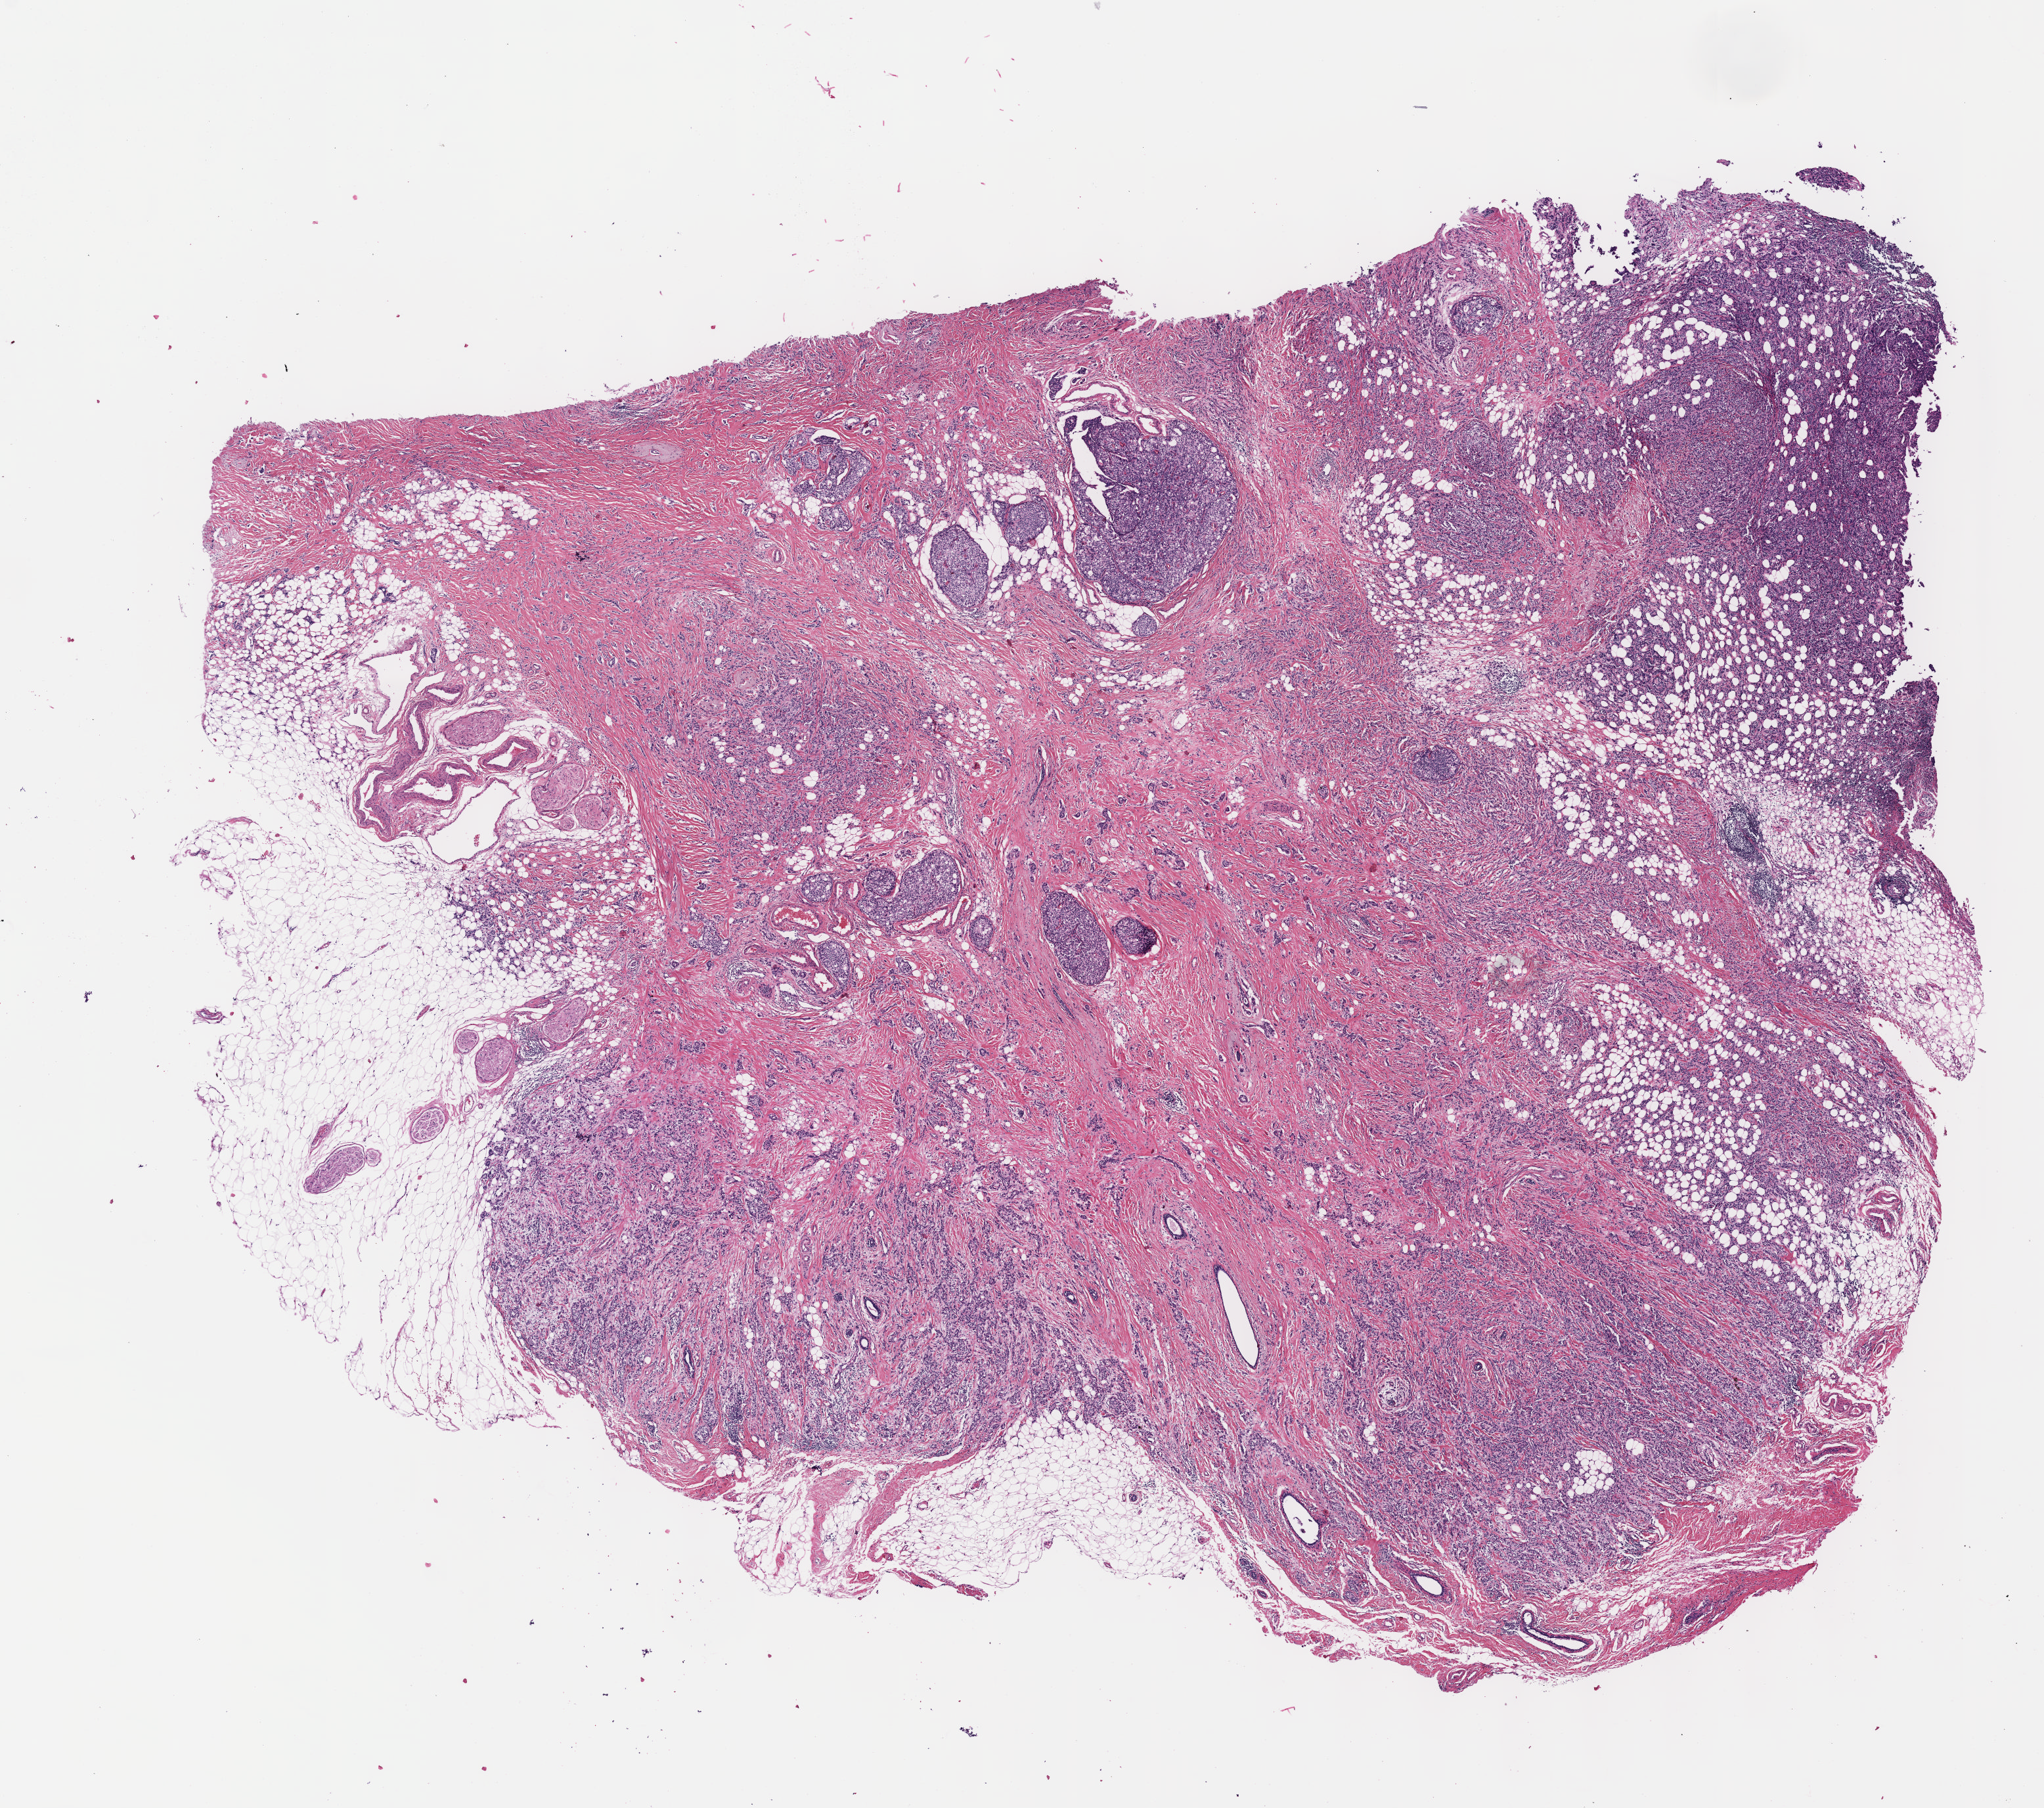
Whole-slide histology image, Hematoxylin and eosin (H&E) stained — whole scanned area (about 12.6 x 11.1 mm, acquisition: 40x scan) shown as a low-resolution overview, formalin-fixed paraffin-embedded (FFPE) diagnostic section, sample: primary tumour, breast. Patient: female, age at initial diagnosis 54 years.
Lymph nodes positive (case pathology): 1 of 17 examined. Laterality: left. AJCC pathologic stage: IIIA (7th edition). Diagnosis: Infiltrating duct carcinoma, NOS.